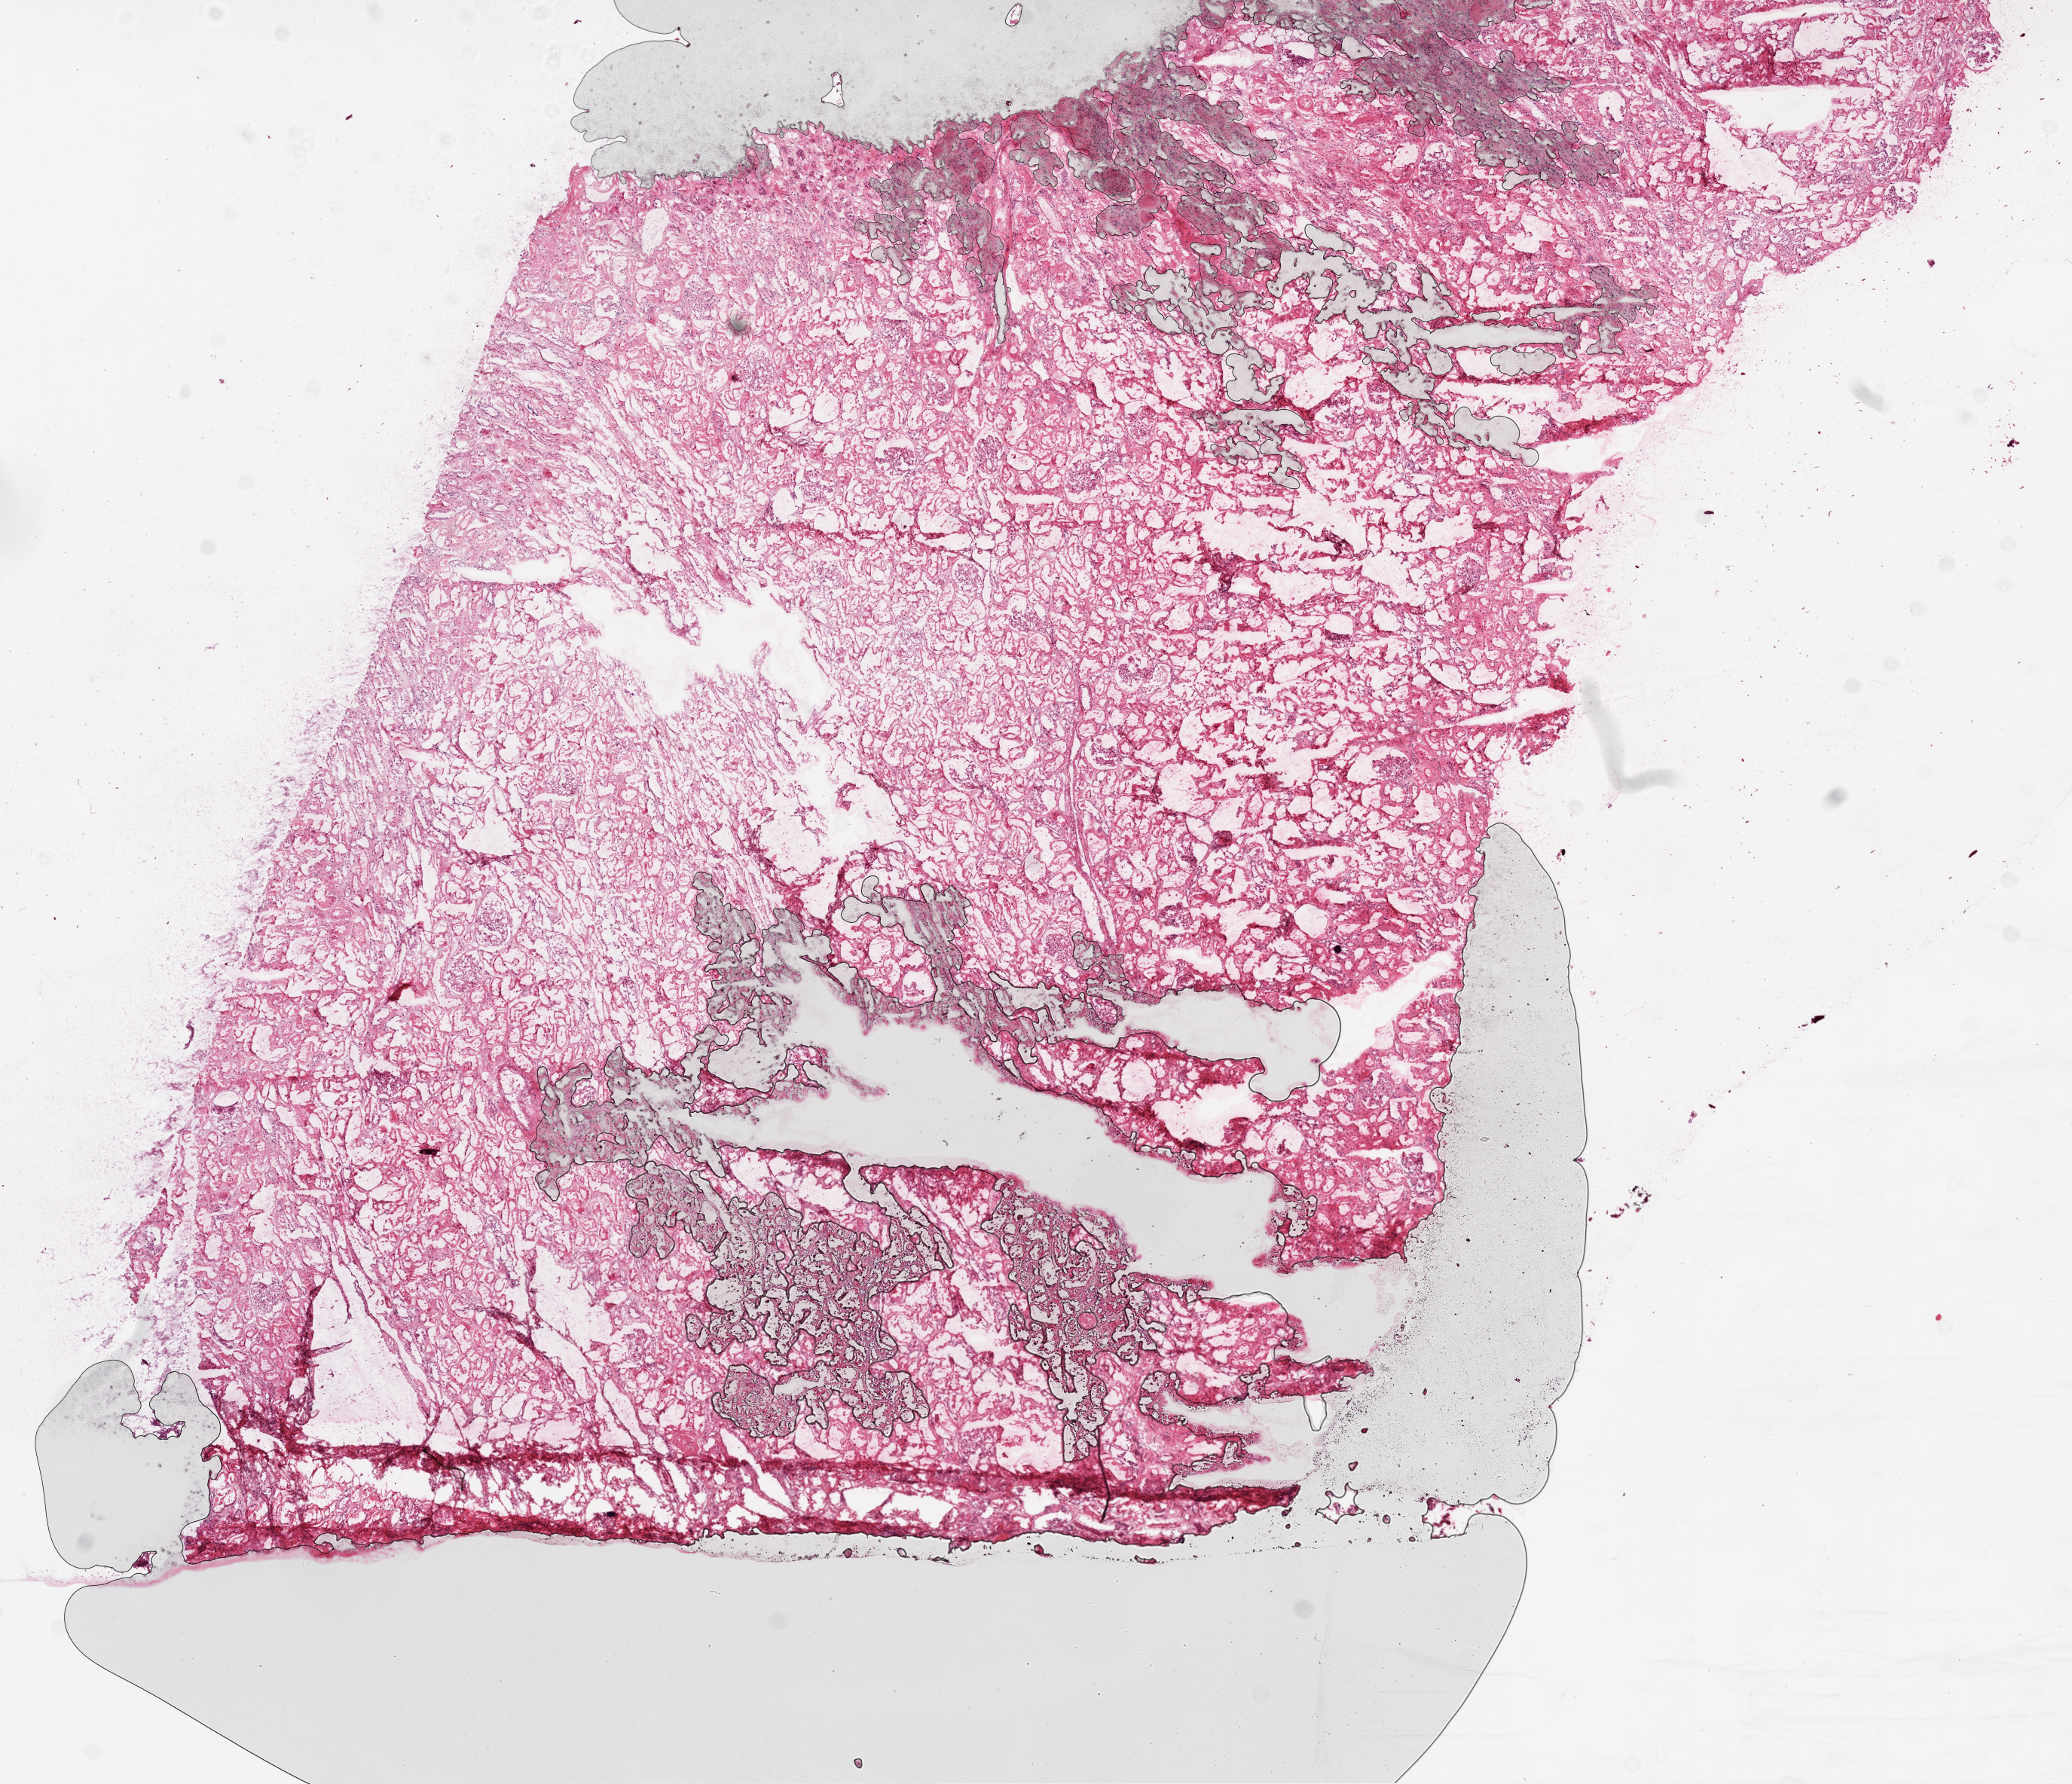
Whole-slide histology image, Hematoxylin and eosin (H&E) stained — whole scanned area (about 11.0 x 9.5 mm, from a 20x scan) shown as a low-resolution overview; frozen section from the top of the tissue portion; solid tissue normal (non-tumour tissue) sample from the kidney. Patient: male, age at initial diagnosis 50 years.
This section: solid tissue normal (non-tumour) sample from the same patient. Patient diagnosis: Clear cell adenocarcinoma, NOS.